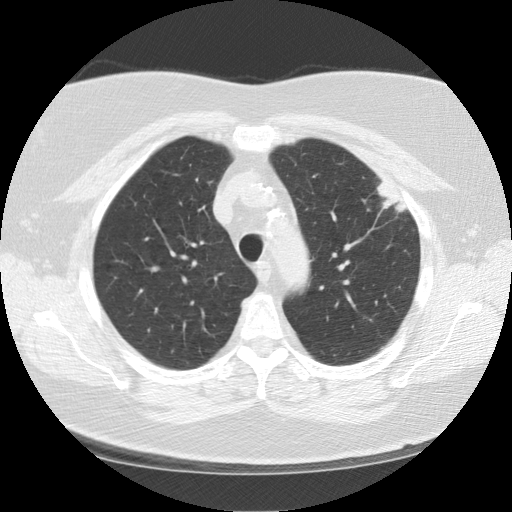
Low-dose screening chest CT, one axial slice; 120 kVp; lung window (W 1500 / L -600 HU); 2.5 mm slice thickness; 512 × 512 image matrix, field of view 350 × 350 mm.
Annotated regions visible in this slice (manually delineated by an expert):
- lesion 1 (tumor, upper lobe of left lung): bounding box <377,182,408,212> (left, top, right, bottom; pixels)